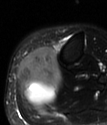
MRI of an extremity soft-tissue mass, one axial slice; slice 26 of 78 in the series (ordered by position); T2-weighted fat-saturated; MR volume resampled by the dataset authors to the PET/CT grid (not the native acquisition matrix); 3.27 mm slice thickness; 107 × 125 image matrix, field of view 104 × 122 mm. Female patient. Case-level facts recorded for this patient, not image findings: histological type: extraskeletal high grade osteogenic sarcoma; grade: high; site of the primary tumour: left calf.
Annotated regions visible in this slice (expert contour drawn on MRI and transferred to this co-registered scan by the dataset authors):
- gross tumour volume (mass): box from (x=17, y=47) to (x=61, y=105) px